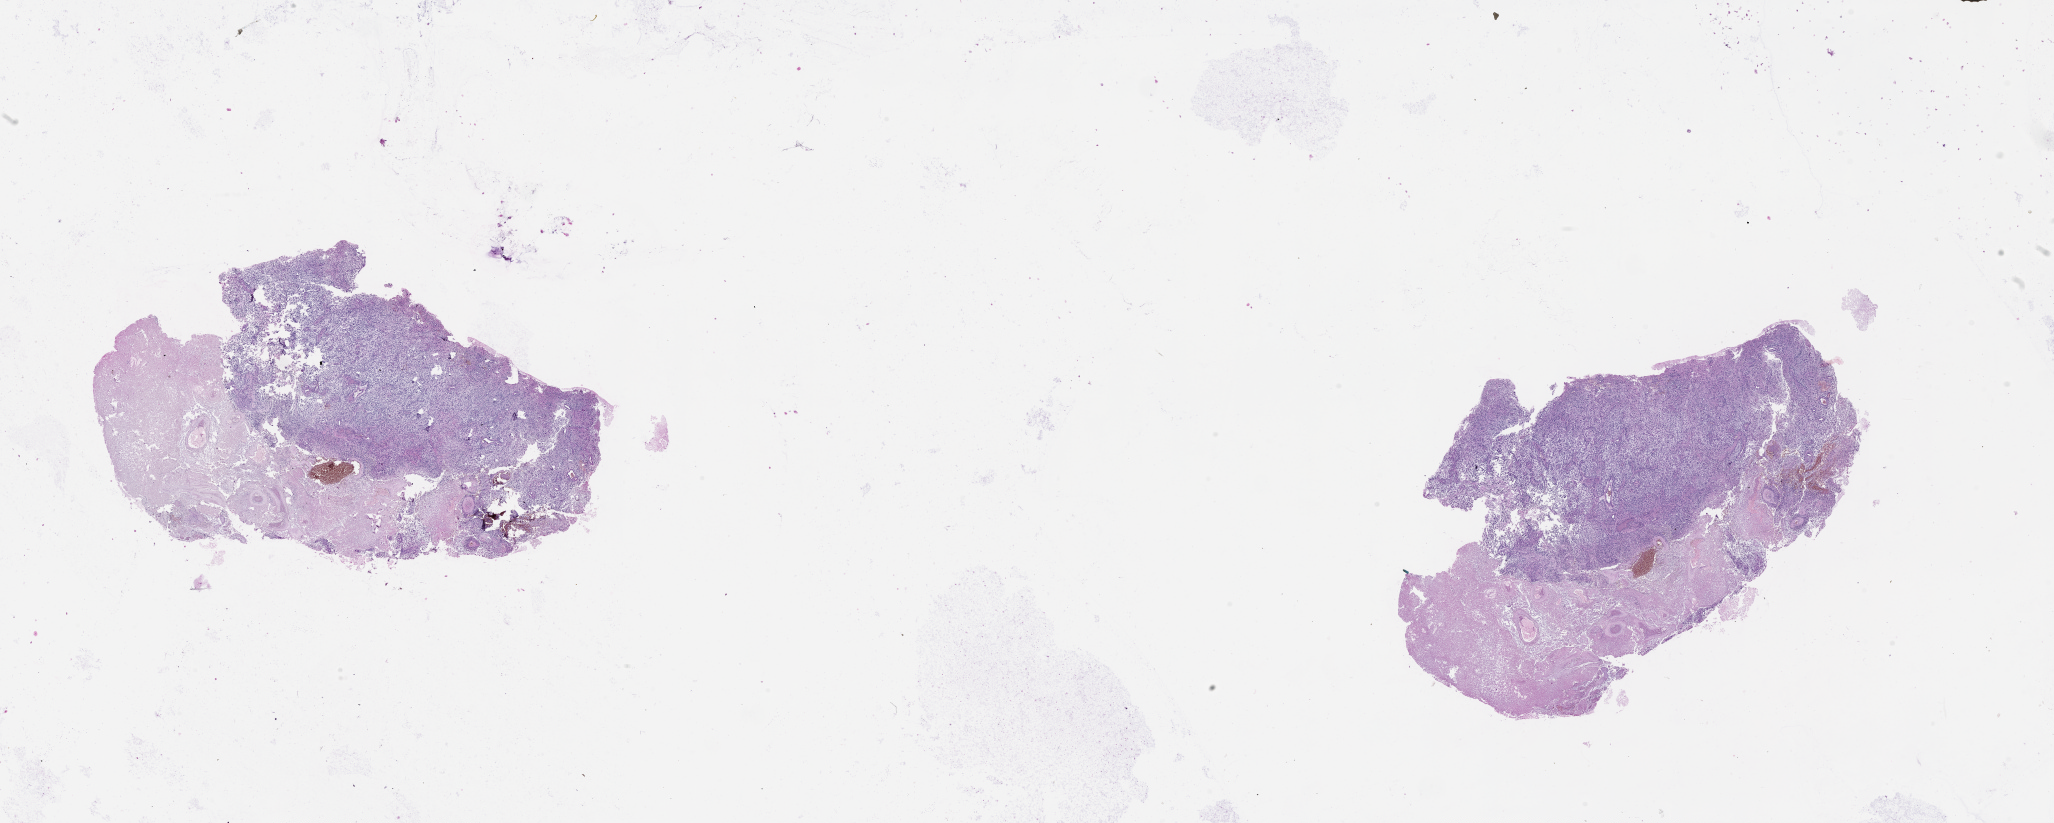
Whole-slide histology image, H&E-stained — low-resolution overview of the scanned area, about 33.1 x 13.3 mm (slide scanned at 20x). Brain, tumour tissue. Male, 65 y/o.
- primary tumour site (as recorded): parietal lobe
- histologic diagnosis: Glioblastoma